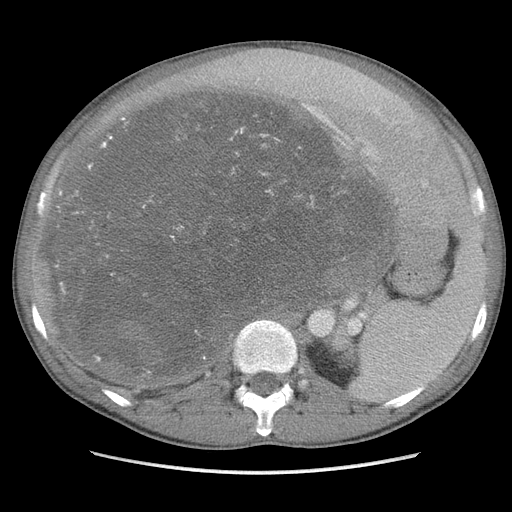
Contrast-enhanced abdominal CT, one axial slice. Position 67 of 115 along the scan axis. Soft-tissue window (W 400 / L 40 HU). 5 mm slice thickness. 512 × 512 image matrix, field of view 360 × 360 mm. Male patient. Case-level facts recorded for this patient, not image findings: diagnosis: adrenocortical carcinoma; tumour side: right adrenal; Ki-67 index: 13 %; stage (as recorded): 3.
Outlined on this slice (semi-automatic segmentation, software-assisted and operator-edited):
- mass: bounding box <60,91,388,384> (left, top, right, bottom; pixels)